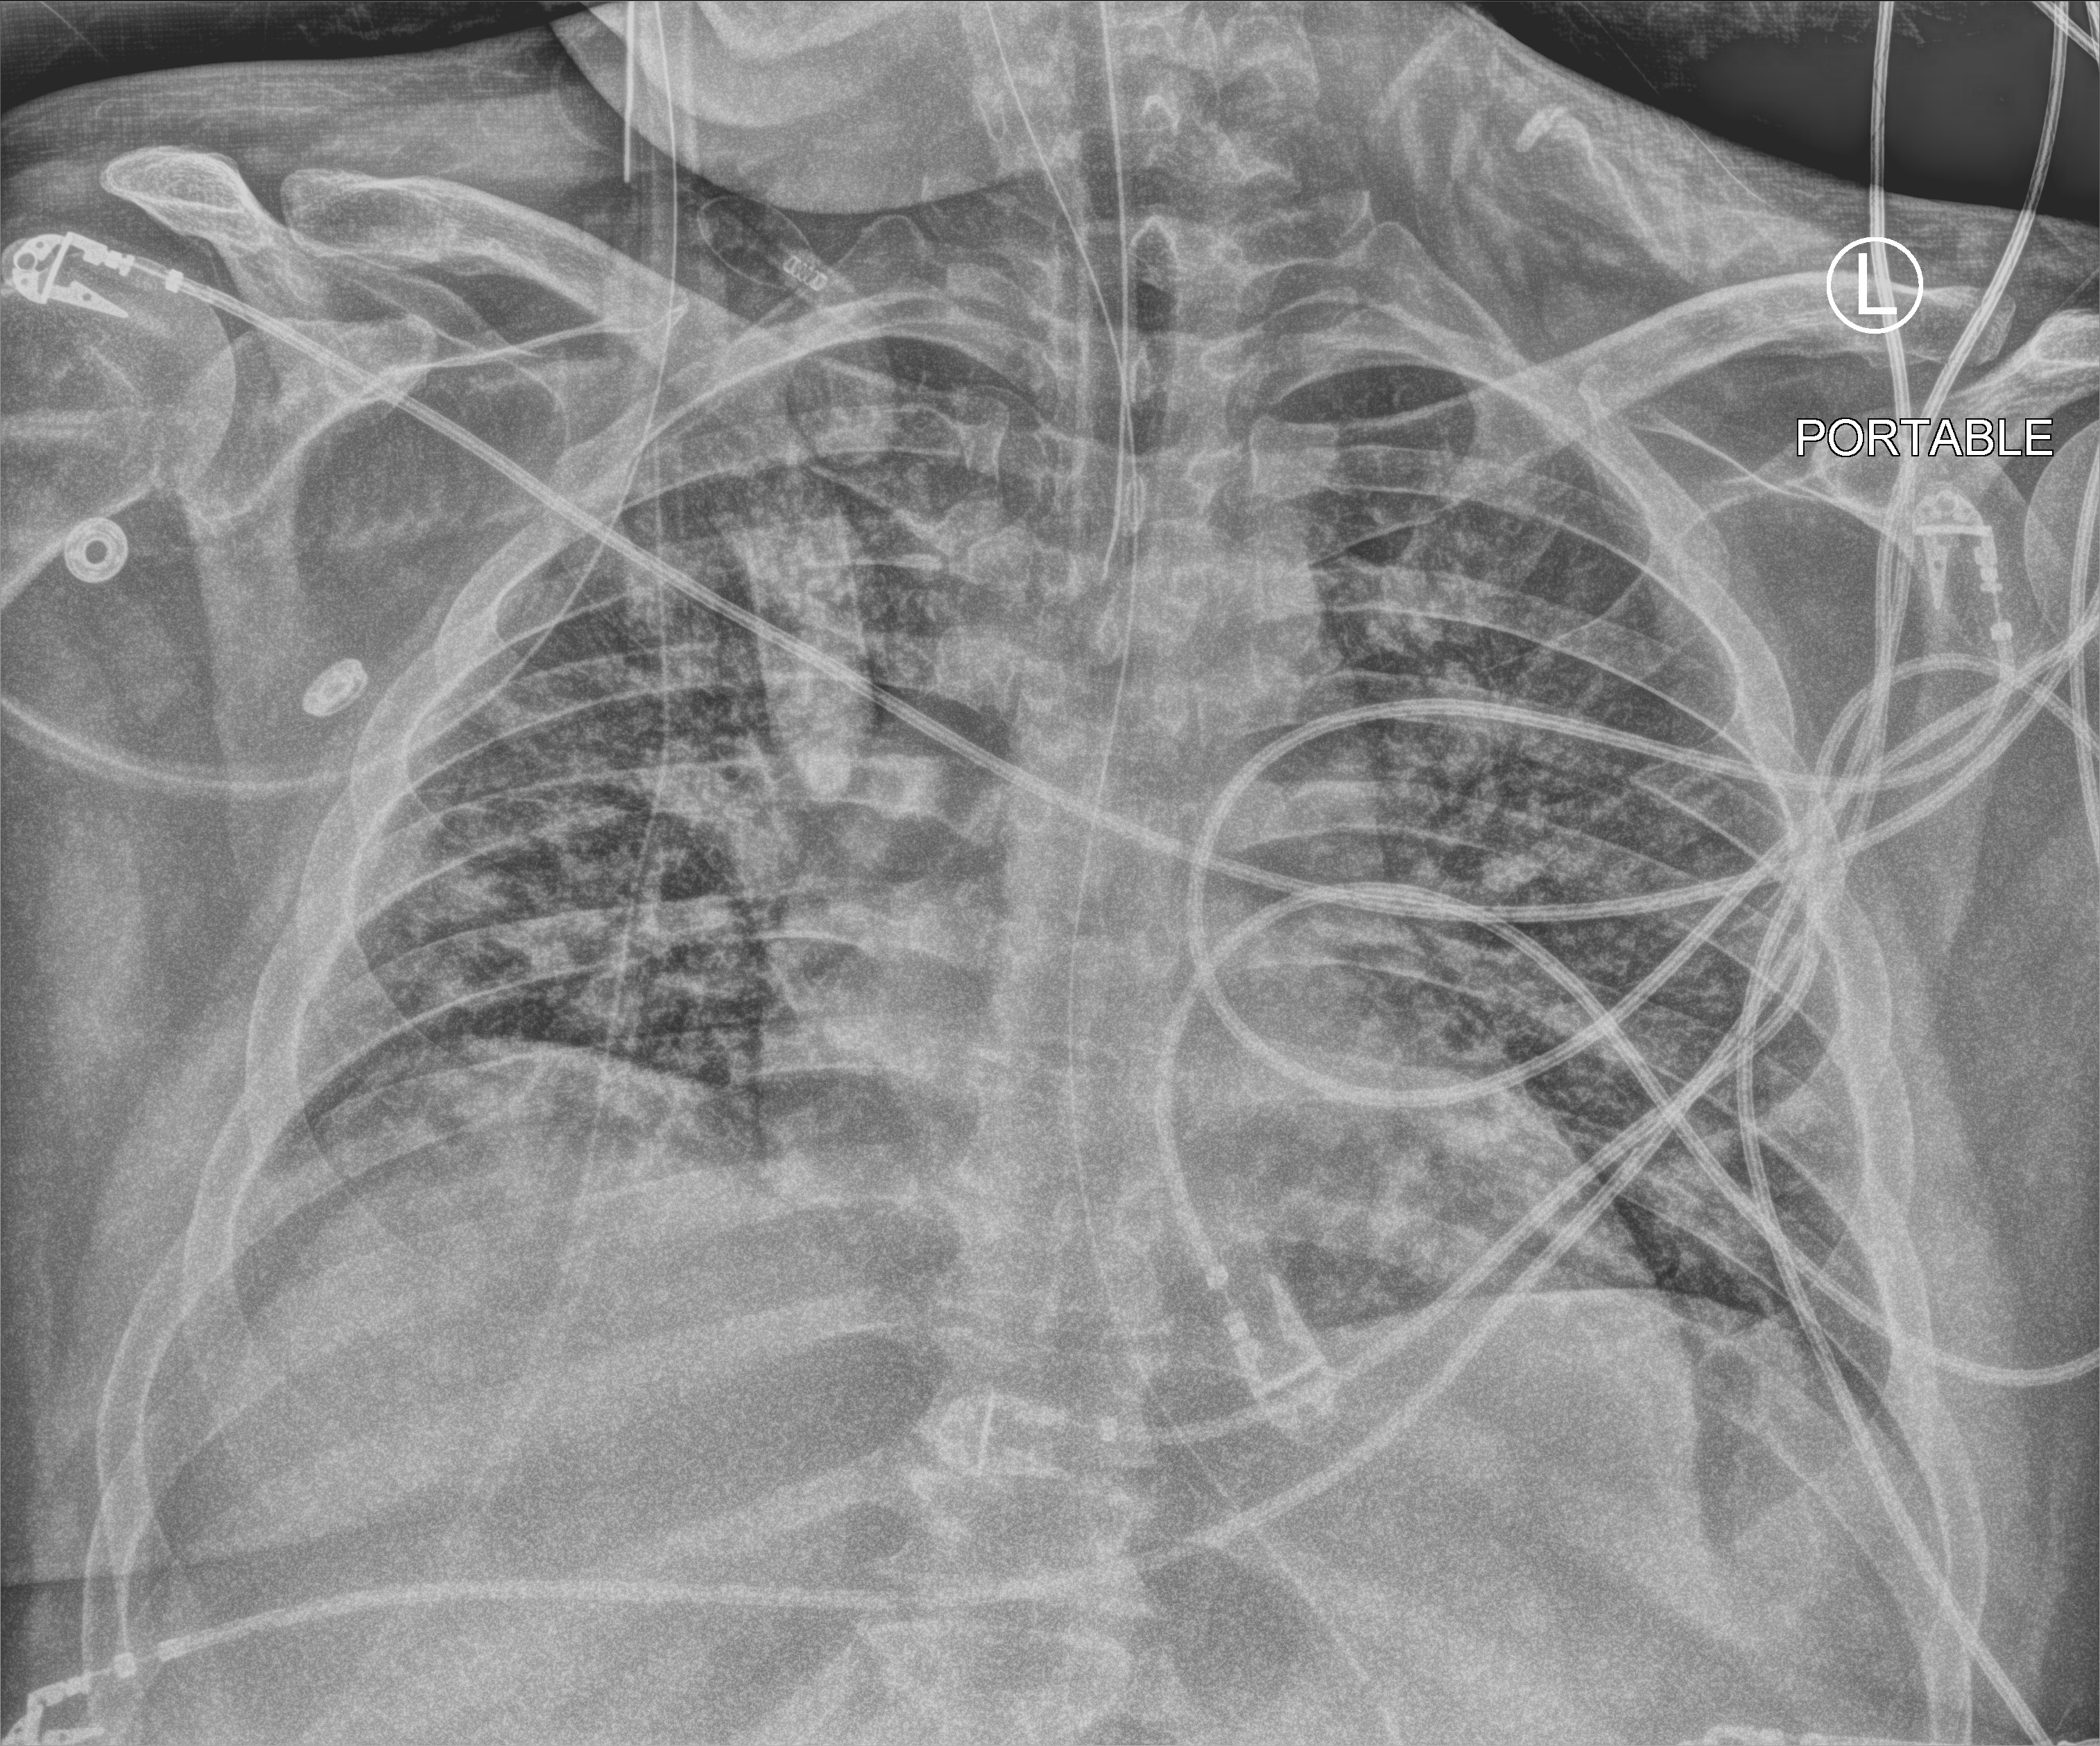
Chest X-ray (portable). Patient hospitalised with COVID-19, aged 18–59 years.
From the hospital-stay record, not from the radiograph (when in the stay this image was taken is not recorded): mechanically ventilated during this hospital stay: yes; admitted to intensive care during this hospital stay: yes.